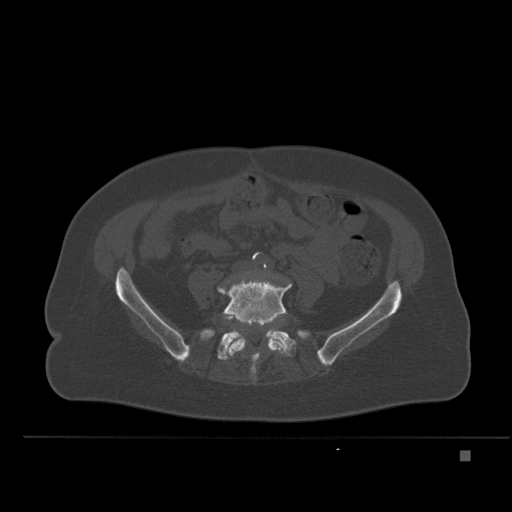
CT including the spine, one axial slice. Slice 159 of 477 in the series (ordered by position). Bone window (W 1800 / L 400 HU). 1.5 mm slice thickness. 512 × 512 image matrix. Female patient, age 74 years. Case-level facts recorded for this patient, not image findings: primary cancer: colon.
Outlined on this slice (semi-automatically segmented with operator editing):
- L5 vertebra: bounding box (x1, y1, x2, y2) in pixels: (218, 277, 293, 357)